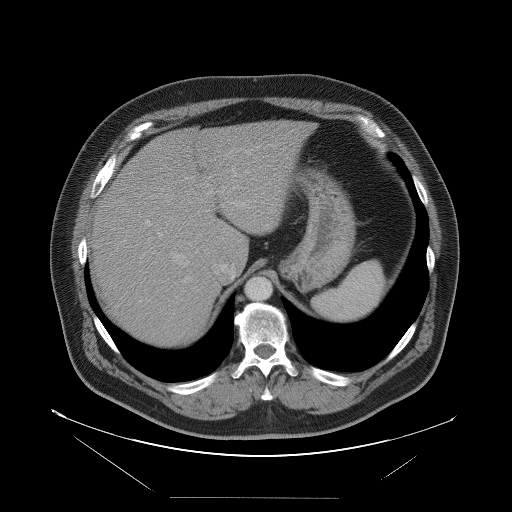
Contrast-enhanced abdominal CT, one axial slice. Position 75 of 114 along the scan axis. Soft-tissue window (W 400 / L 40 HU). 5 mm slice thickness. 512 × 512 image matrix. Male patient, age 61 years. From the clinical record (not read from this slice): diagnosis: colorectal cancer liver metastases, imaged before liver resection; multiple liver metastases: no; largest metastasis: 6.5 cm; chemotherapy before resection: no.
Structures marked on this image (outlined manually by an expert reader):
- hepatic veins: box from (x=158, y=167) to (x=256, y=283) px
- liver: (x=90, y=121)–(x=311, y=346)
- planned liver remnant (the part of the liver to remain after resection): (x=146, y=121)–(x=311, y=266)
- portal vein (with intrahepatic branches): (x=141, y=150)–(x=250, y=302)